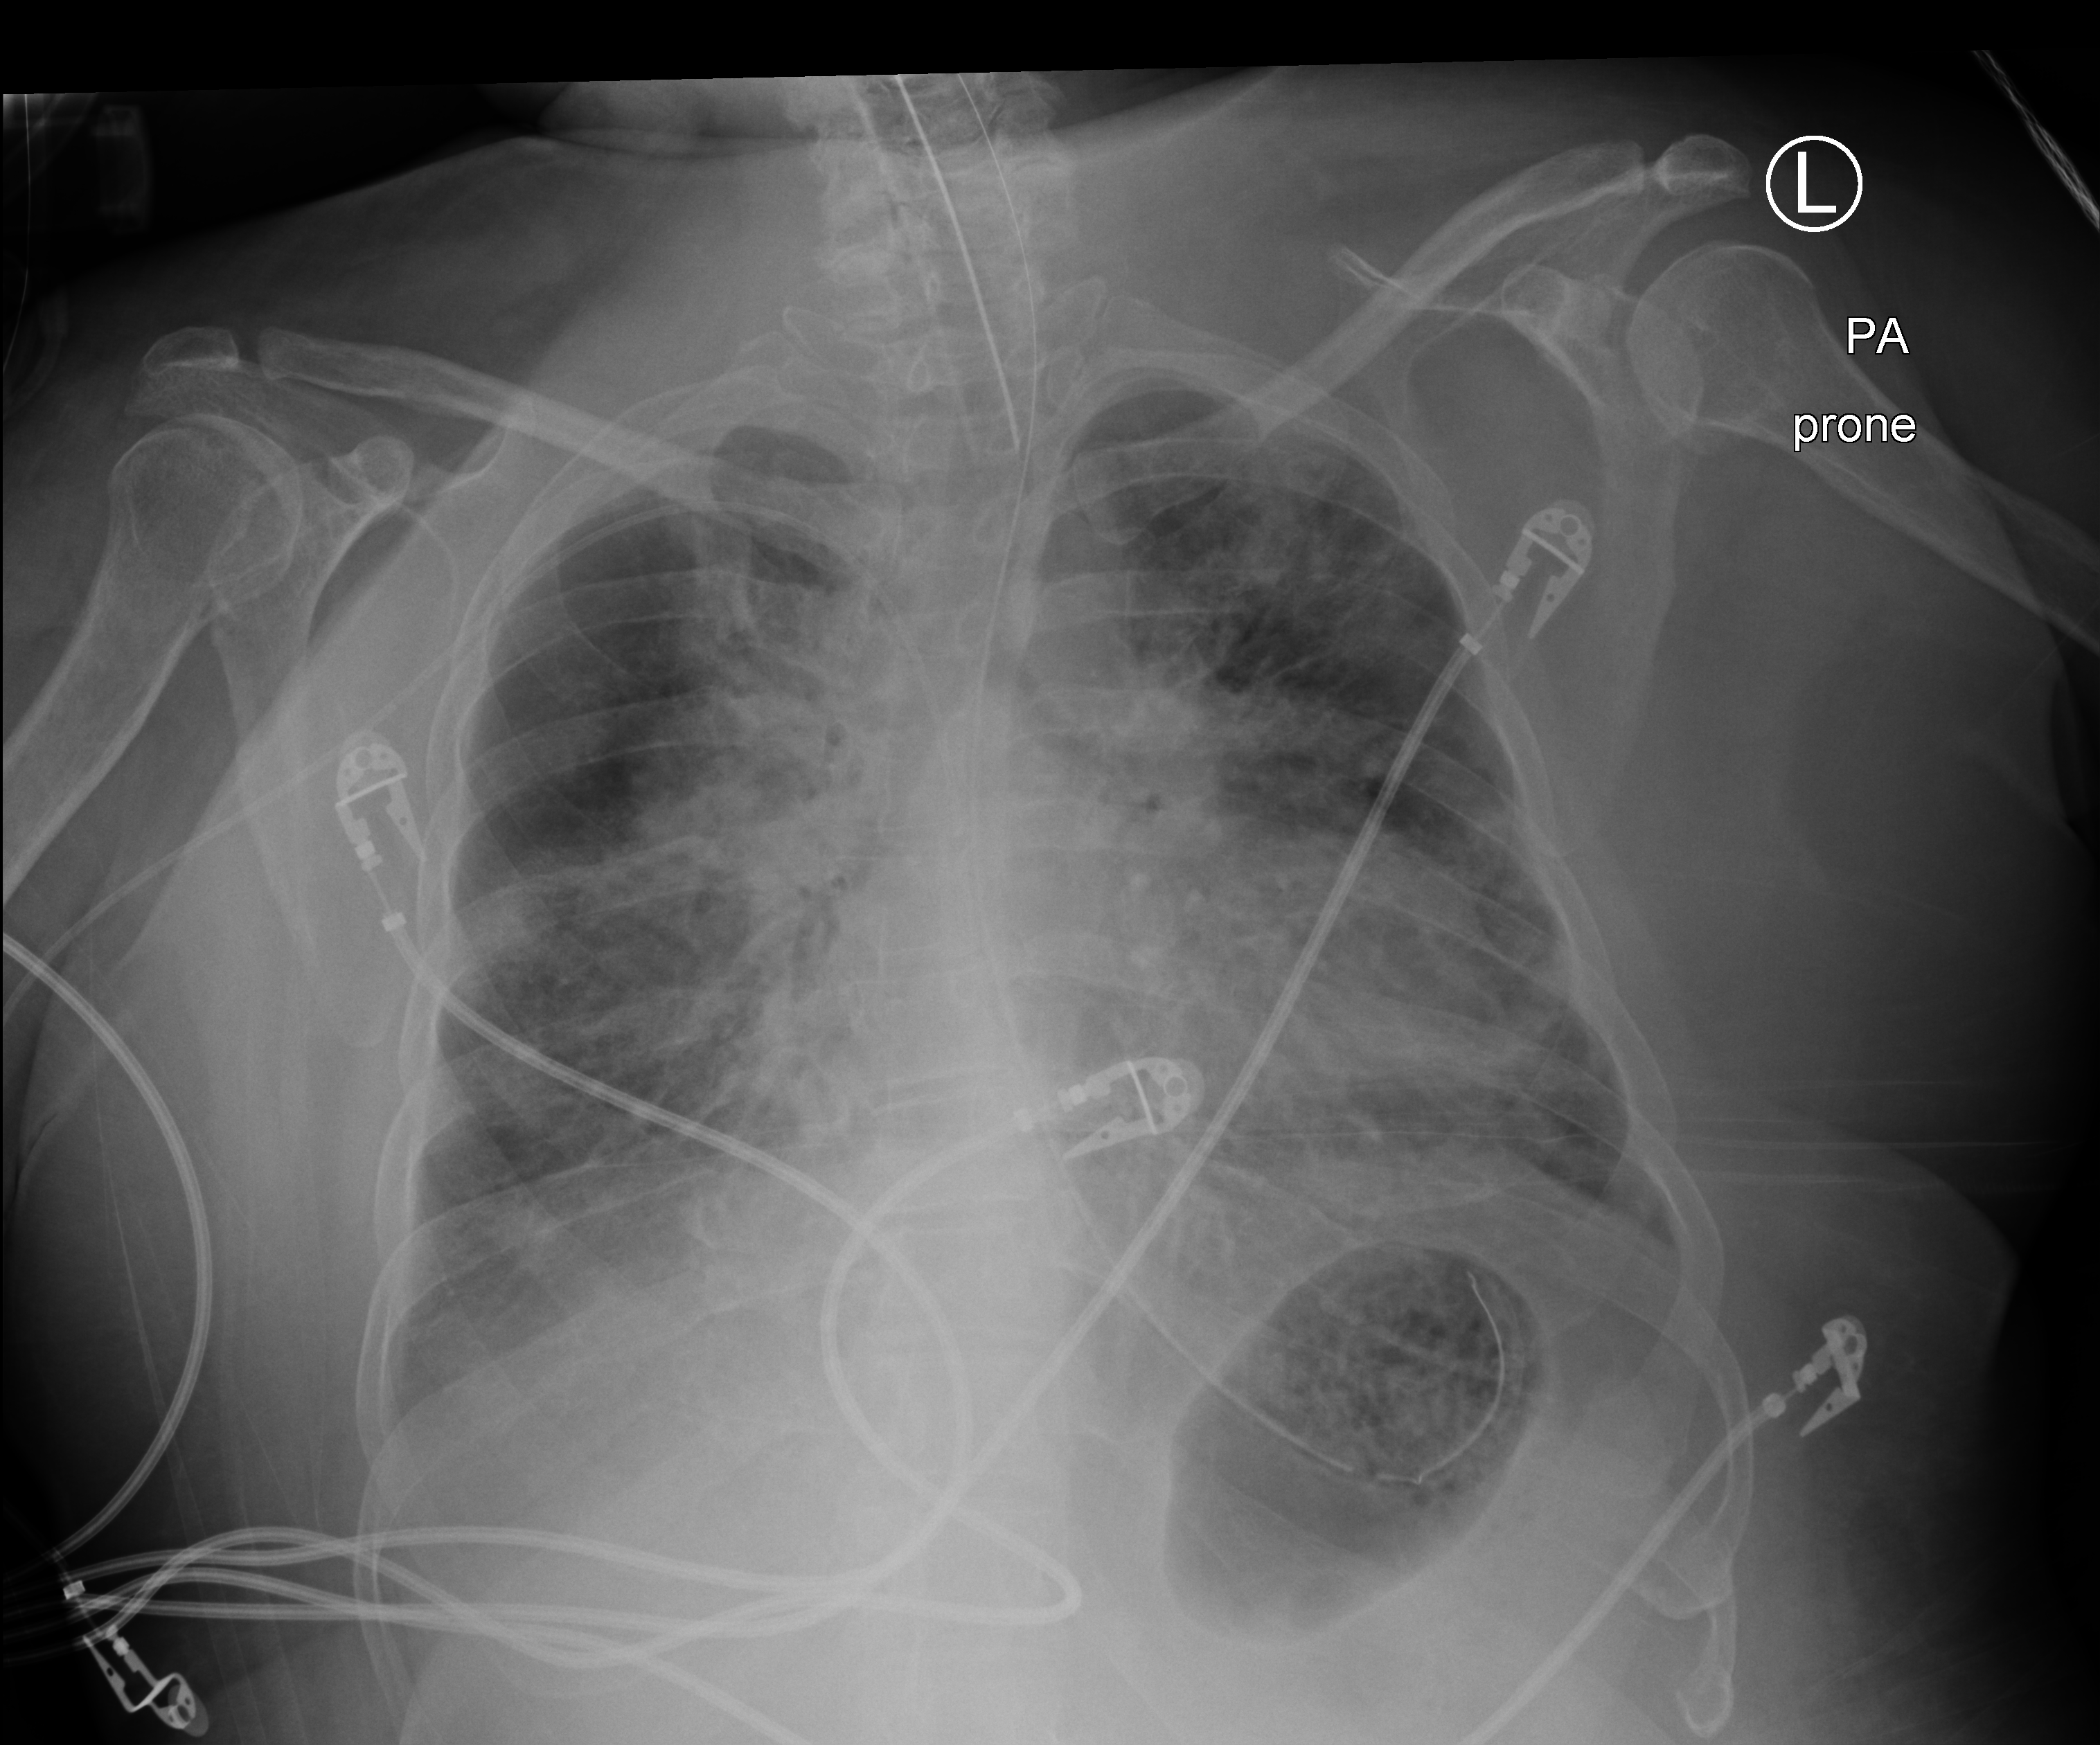
Bedside chest radiograph (computed radiography). Patient hospitalised with COVID-19, aged 18–59 years.
Admission-level facts for this patient (not findings on this image; timing relative to this image not recorded):
- admitted to intensive care during this hospital stay: yes
- mechanically ventilated during this hospital stay: yes